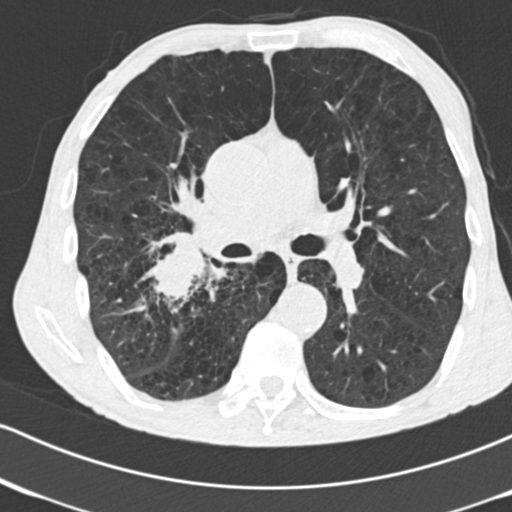
Low-dose screening chest CT, axial slice, second annual screen, lung window (W 1500 / L -600 HU), 2 mm slice thickness, standard (soft-tissue) reconstruction kernel (B30f), 120 kVp. Male participant, aged 64 years at enrolment. Current smoker at enrolment.
• Expert reader's lesion annotation, bounding box [x1, y1, x2, y2] px = [133, 231, 238, 327].
• Reader record for this screening exam (exam-level; its link to the box is not recorded): non-calcified nodule or mass ≥4 mm, 52 × 37 mm, spiculated (stellate) margins, soft tissue attenuation, pre-existing on the prior screen: no.
• Later outcome: lung cancer diagnosed 28 days after this screen — adenocarcinoma, NOS, right lower lobe, stage IV (AJCC 6th edition), 60 mm at pathology.